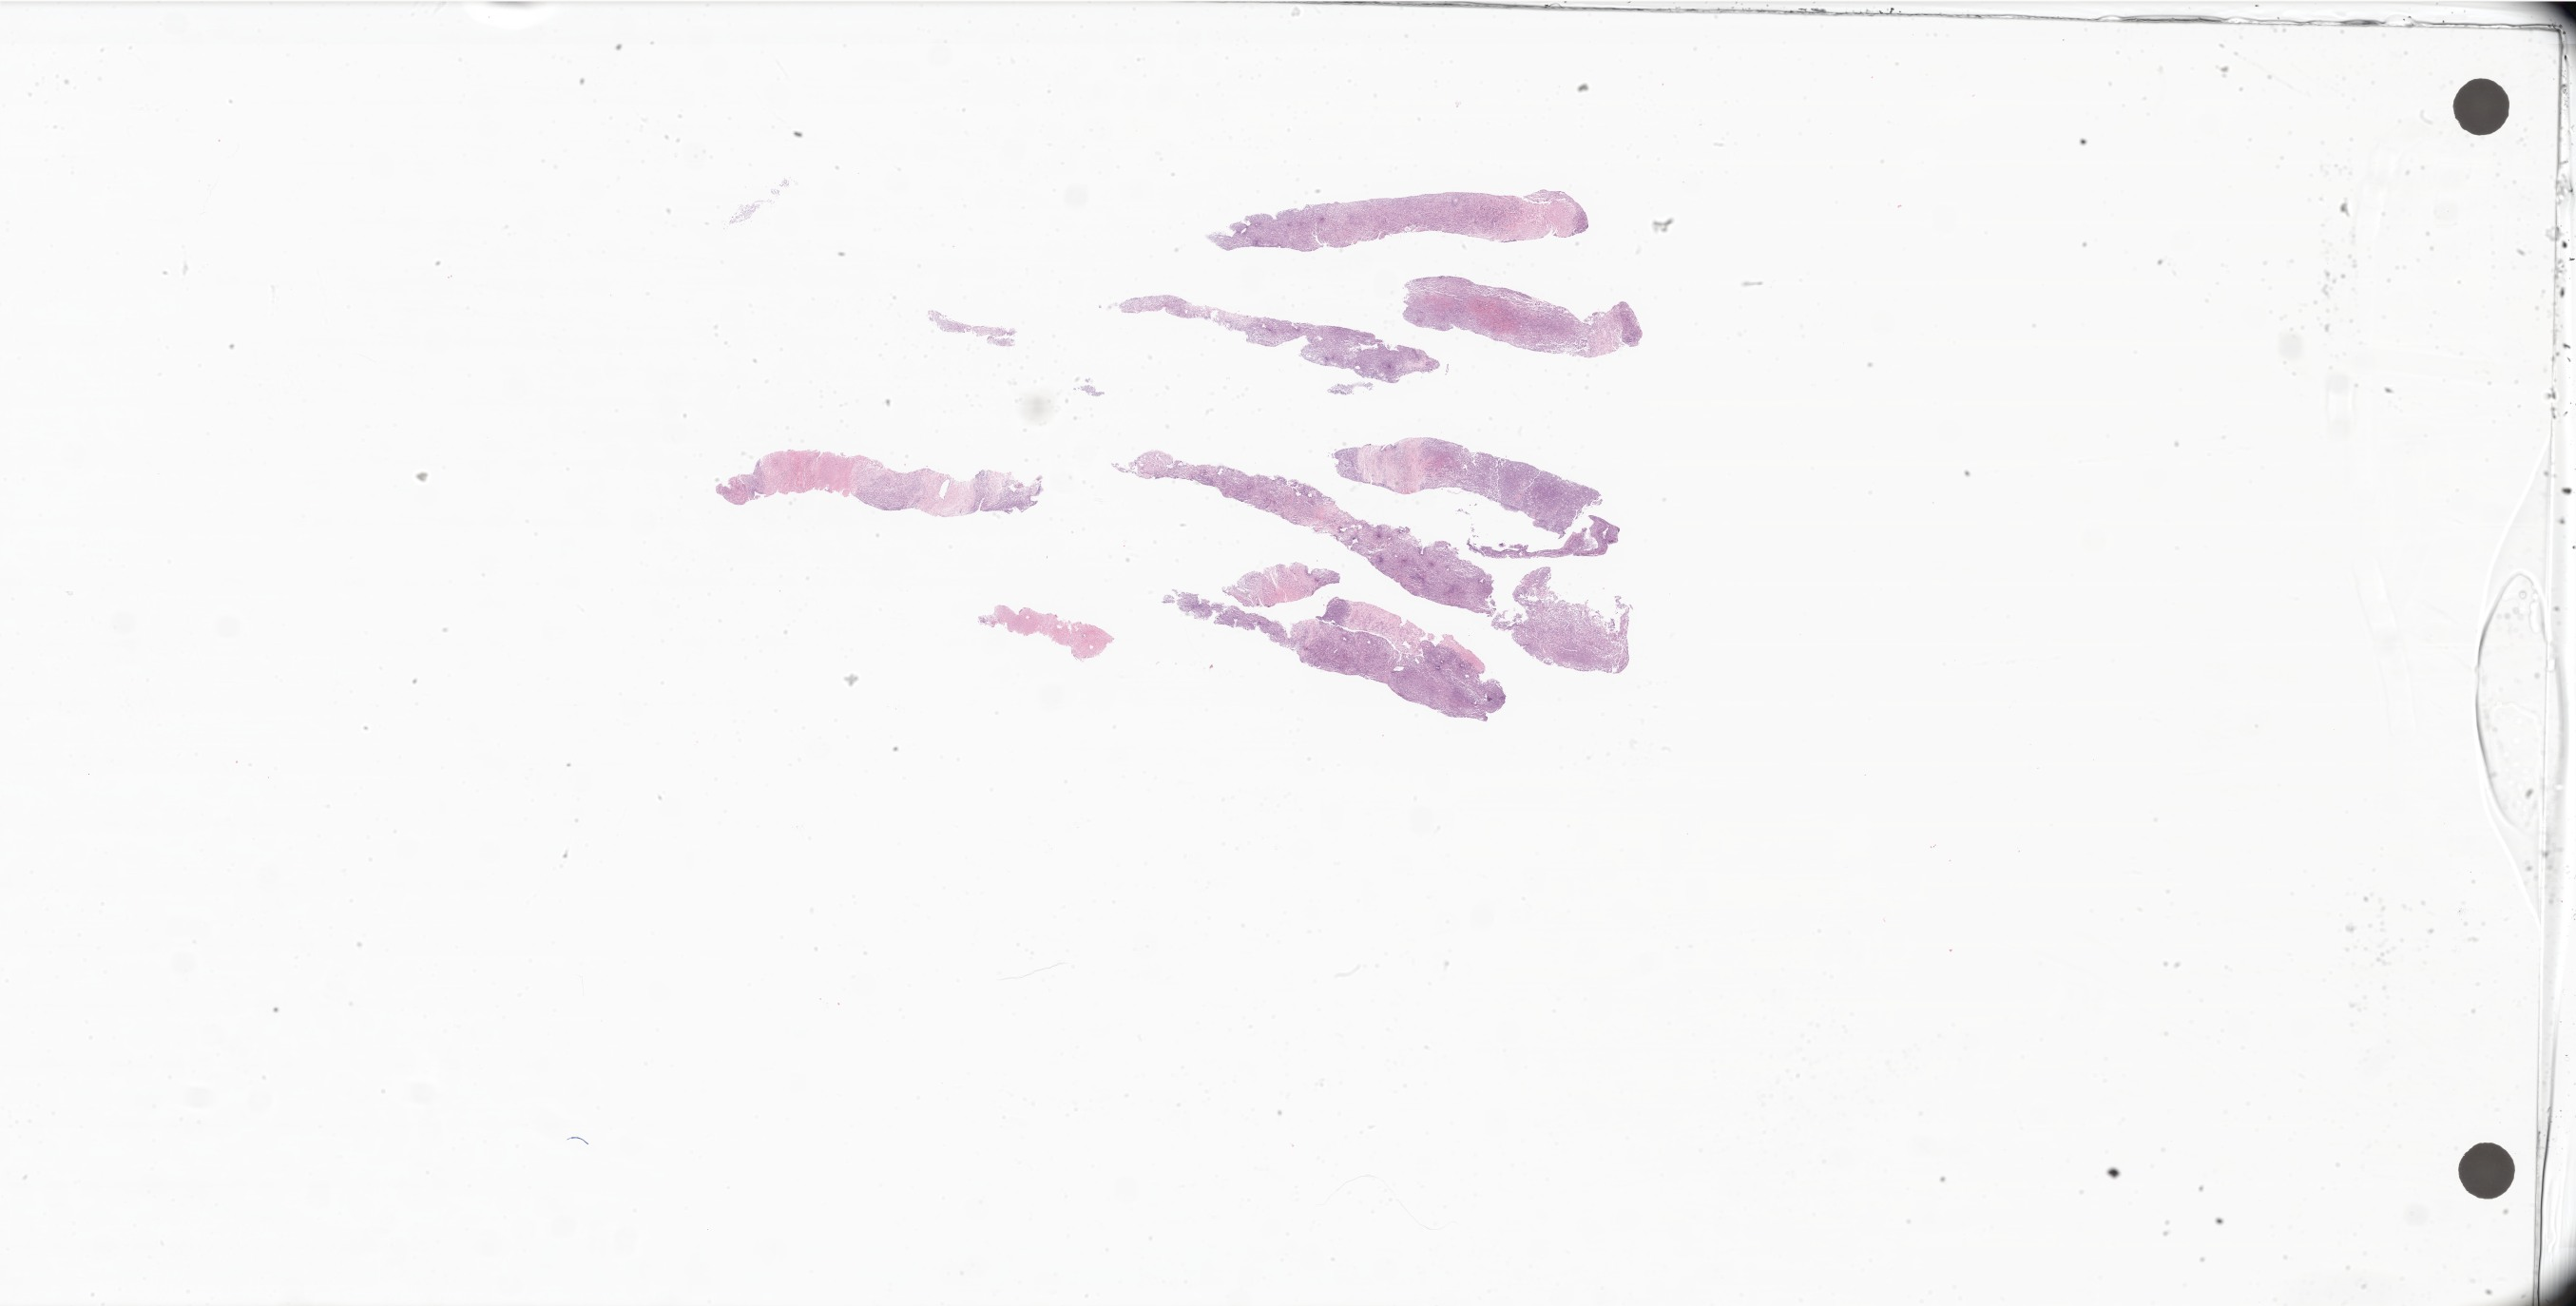
Whole-slide image, H&E stain of tumor tissue from the soft tissue of upper extremity — a low-resolution overview of the entire scanned area, about 45.7 x 23.2 mm. Formalin-fixed, paraffin-embedded (FFPE) tissue. Female patient, age 156 days.
Recorded diagnosis: Rhabdoid tumor, NOS. Tissue or organ of origin (case record): connective, subcutaneous and other soft tissues of upper limb and shoulder.